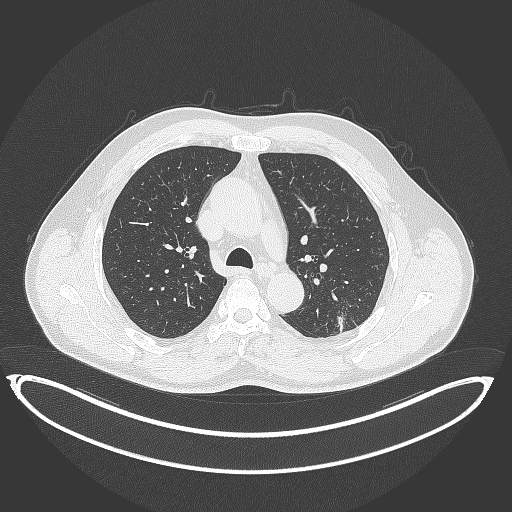
Chest CT, one axial slice. Position 241 of 399 along the scan axis. Reconstruction kernel B70f. Lung window (W 1500 / L -600 HU). 1 mm slice thickness. 512 × 512 image matrix, field of view 469 × 469 mm. Male patient, age 58 years. From the clinical record (not read from this slice): clinical TNM (as recorded): T1c N0 M0.
Structures marked on this image (bounding box drawn by a radiologist):
- lung tumour (recorded histology: adenocarcinoma): box from (x=330, y=307) to (x=355, y=336) px